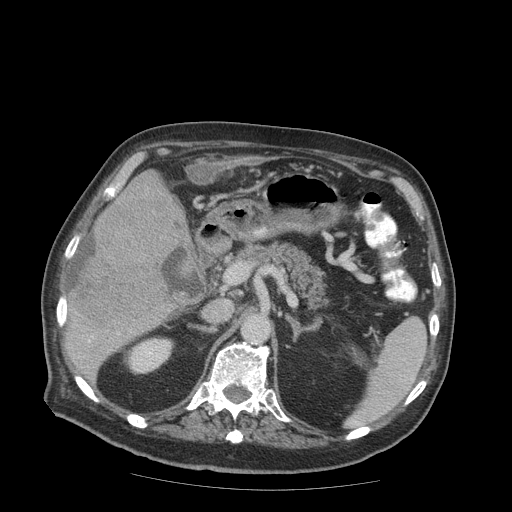
Contrast-enhanced abdominal CT (liver protocol), one axial slice. Position 42 of 99 along the scan axis. Reconstruction kernel STANDARD. 140 kVp. Soft-tissue window (W 400 / L 40 HU). 2.5 mm slice thickness. 512 × 512 image matrix, field of view 420 × 420 mm. Case-level facts recorded for this patient, not image findings: diagnosis: hepatocellular carcinoma (patient treated with transarterial chemoembolisation; whether this scan precedes or follows treatment is not stated here); TNM stage (as recorded): Stage-IIIB; Child-Pugh class: A; tumour differentiation: well differentiated.
Structures marked on this image (semi-automatically segmented with operator editing):
- liver parenchyma outside the tumour (the mass and vessels are separate outlines, so this box may not span the whole liver): bounding box [x1, y1, x2, y2] px = [66, 171, 188, 378]
- mass: [68, 192, 176, 325]
- liver vessels: [88, 340, 91, 342]